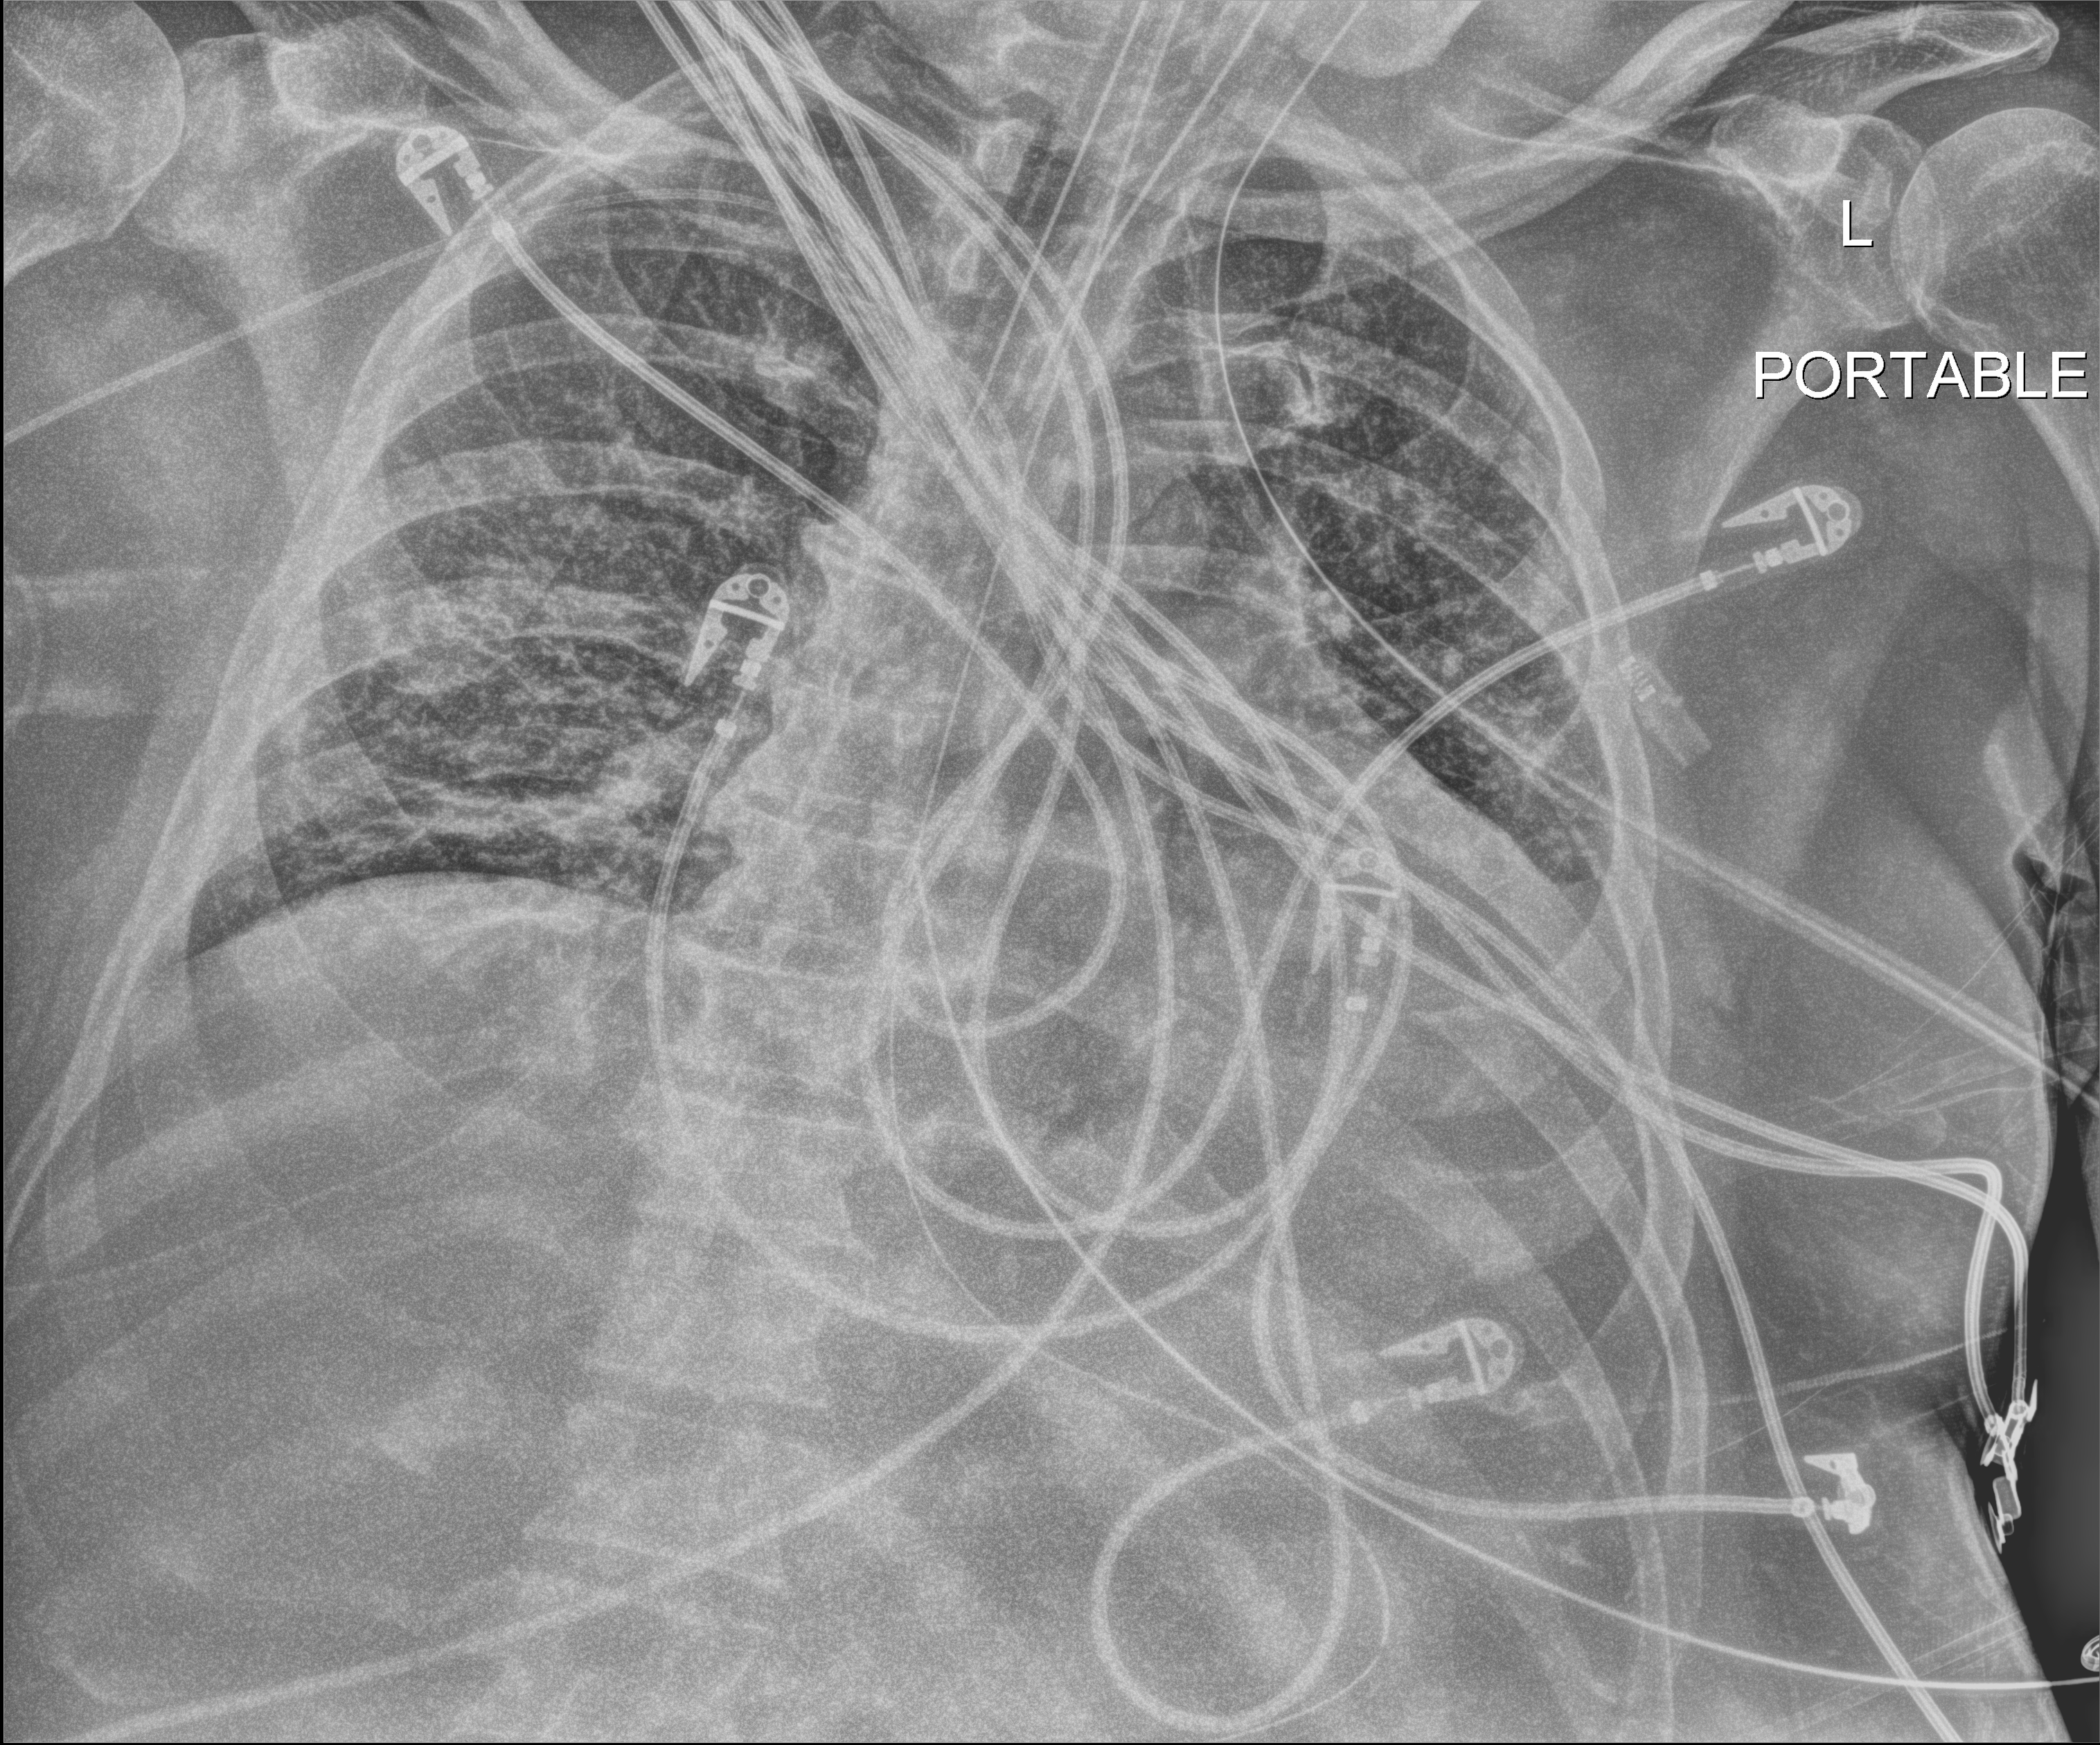
Chest X-ray (portable); anteroposterior (AP) projection. Male patient hospitalised with COVID-19, age 18–59 years.
Hospital-stay facts (about this admission, not read from this image; timing relative to this image not recorded): length of hospital stay: 21 days; smoking status (admission record): former; admitted to intensive care during this hospital stay: yes.